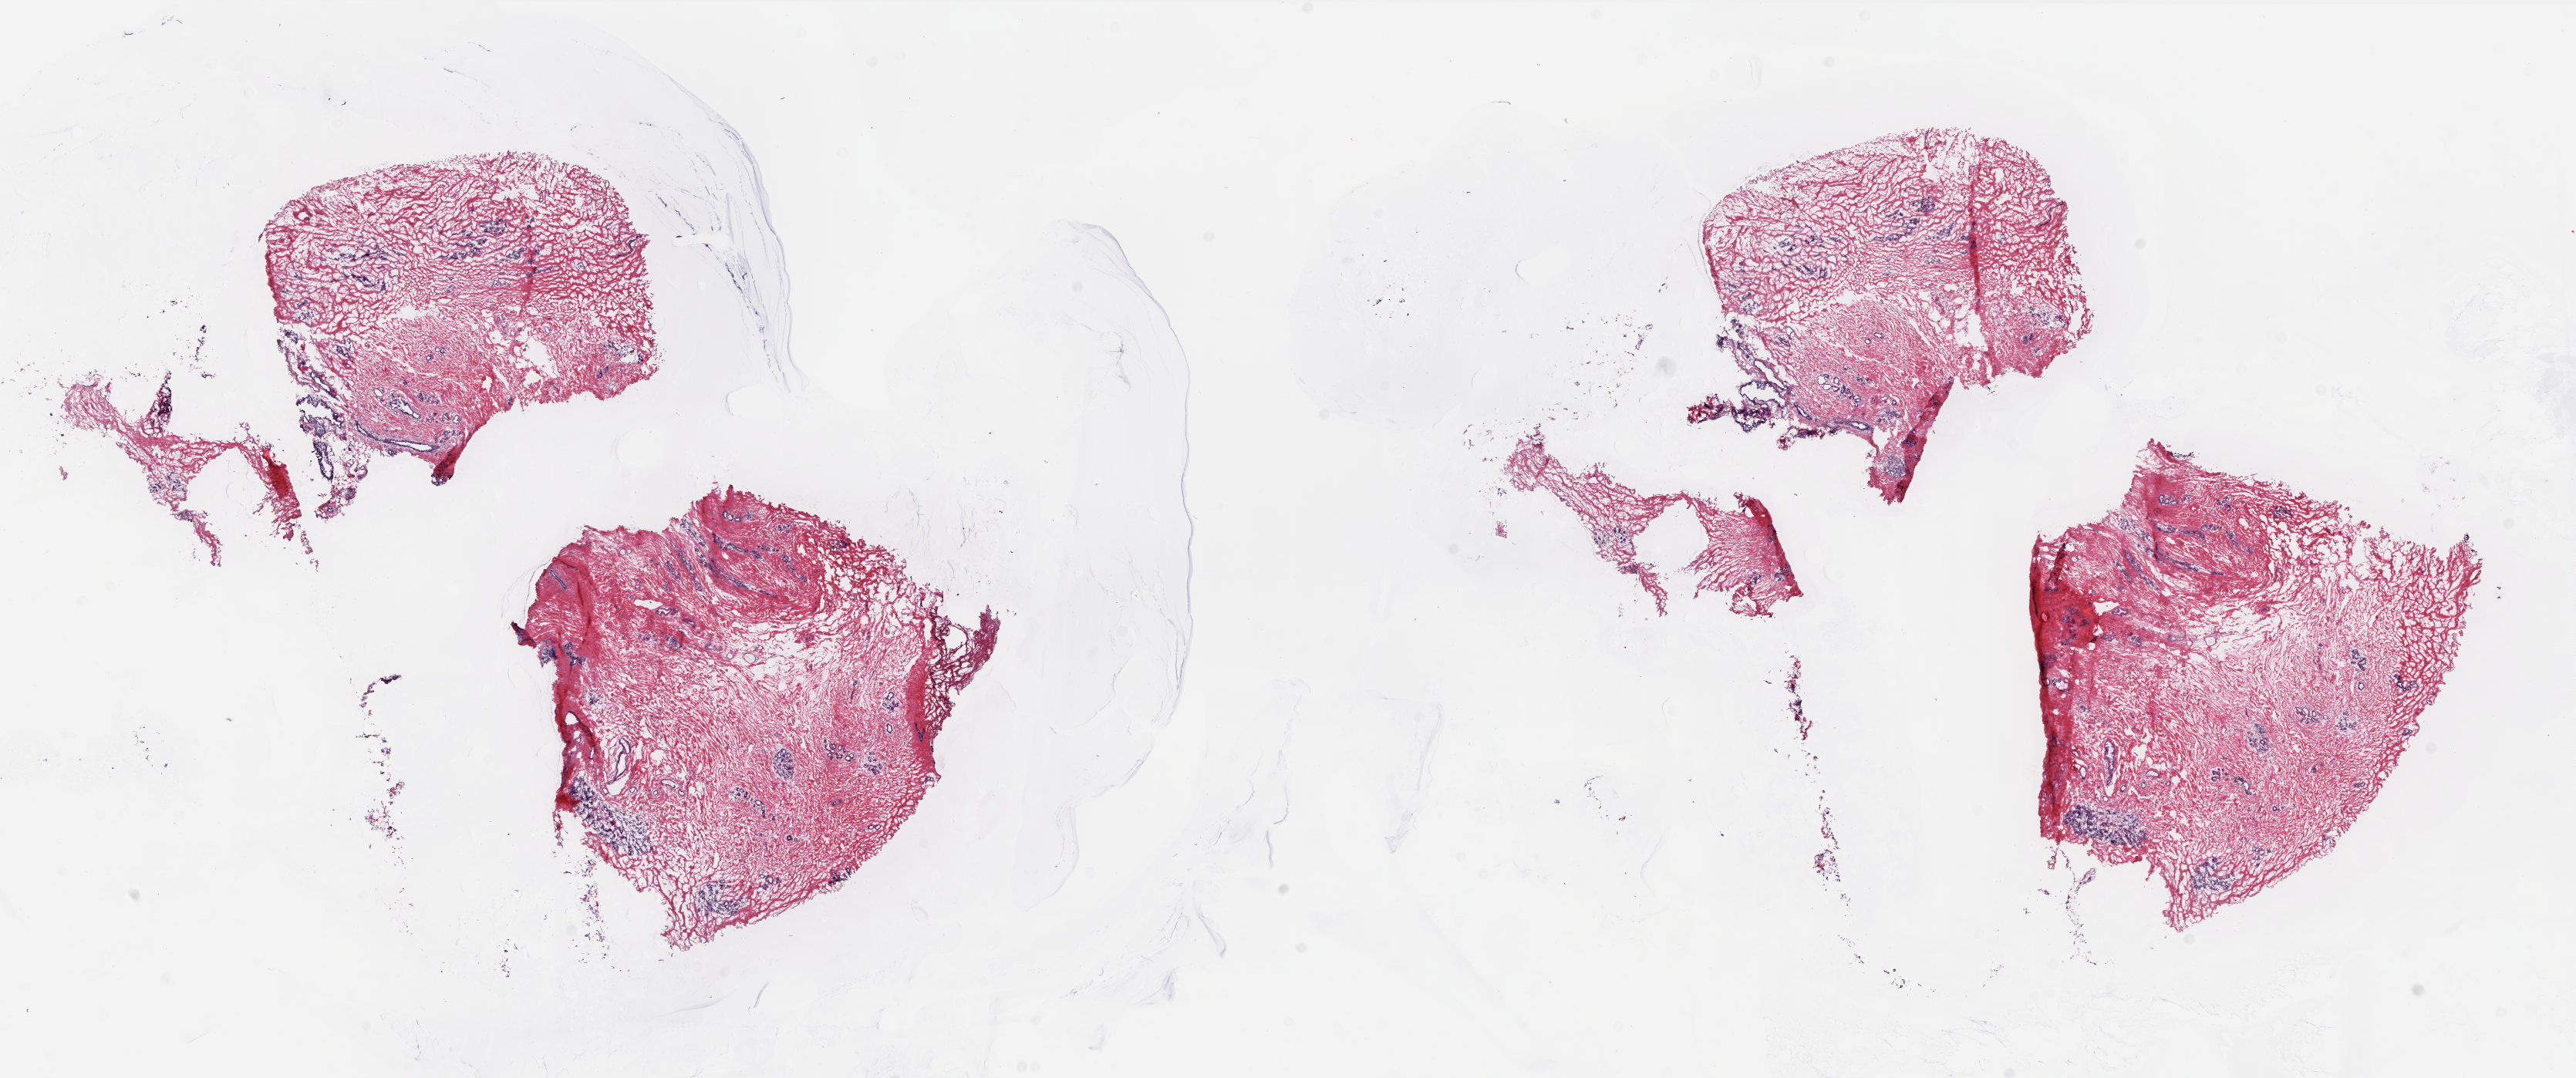
Digitized Hematoxylin and eosin (H&E) stained tissue section (whole slide) — shown as a low-resolution overview of the whole scanned area (about 26.9 x 11.3 mm, slide scanned at 20x); frozen section; breast, solid tissue normal (non-tumour tissue) sample. Female, age 40 years at initial diagnosis. Composition of this section per pathologist review: tumour cells 0%, tumour nuclei 0%, normal cells 18%, stromal cells 82%, necrosis 0%. Inflammatory infiltration, as recorded: lymphocyte infiltration 1%, monocyte infiltration 0%, neutrophil infiltration 0%.
This section: solid tissue normal (non-tumour) sample from the same patient. Patient diagnosis: Lobular carcinoma, NOS.